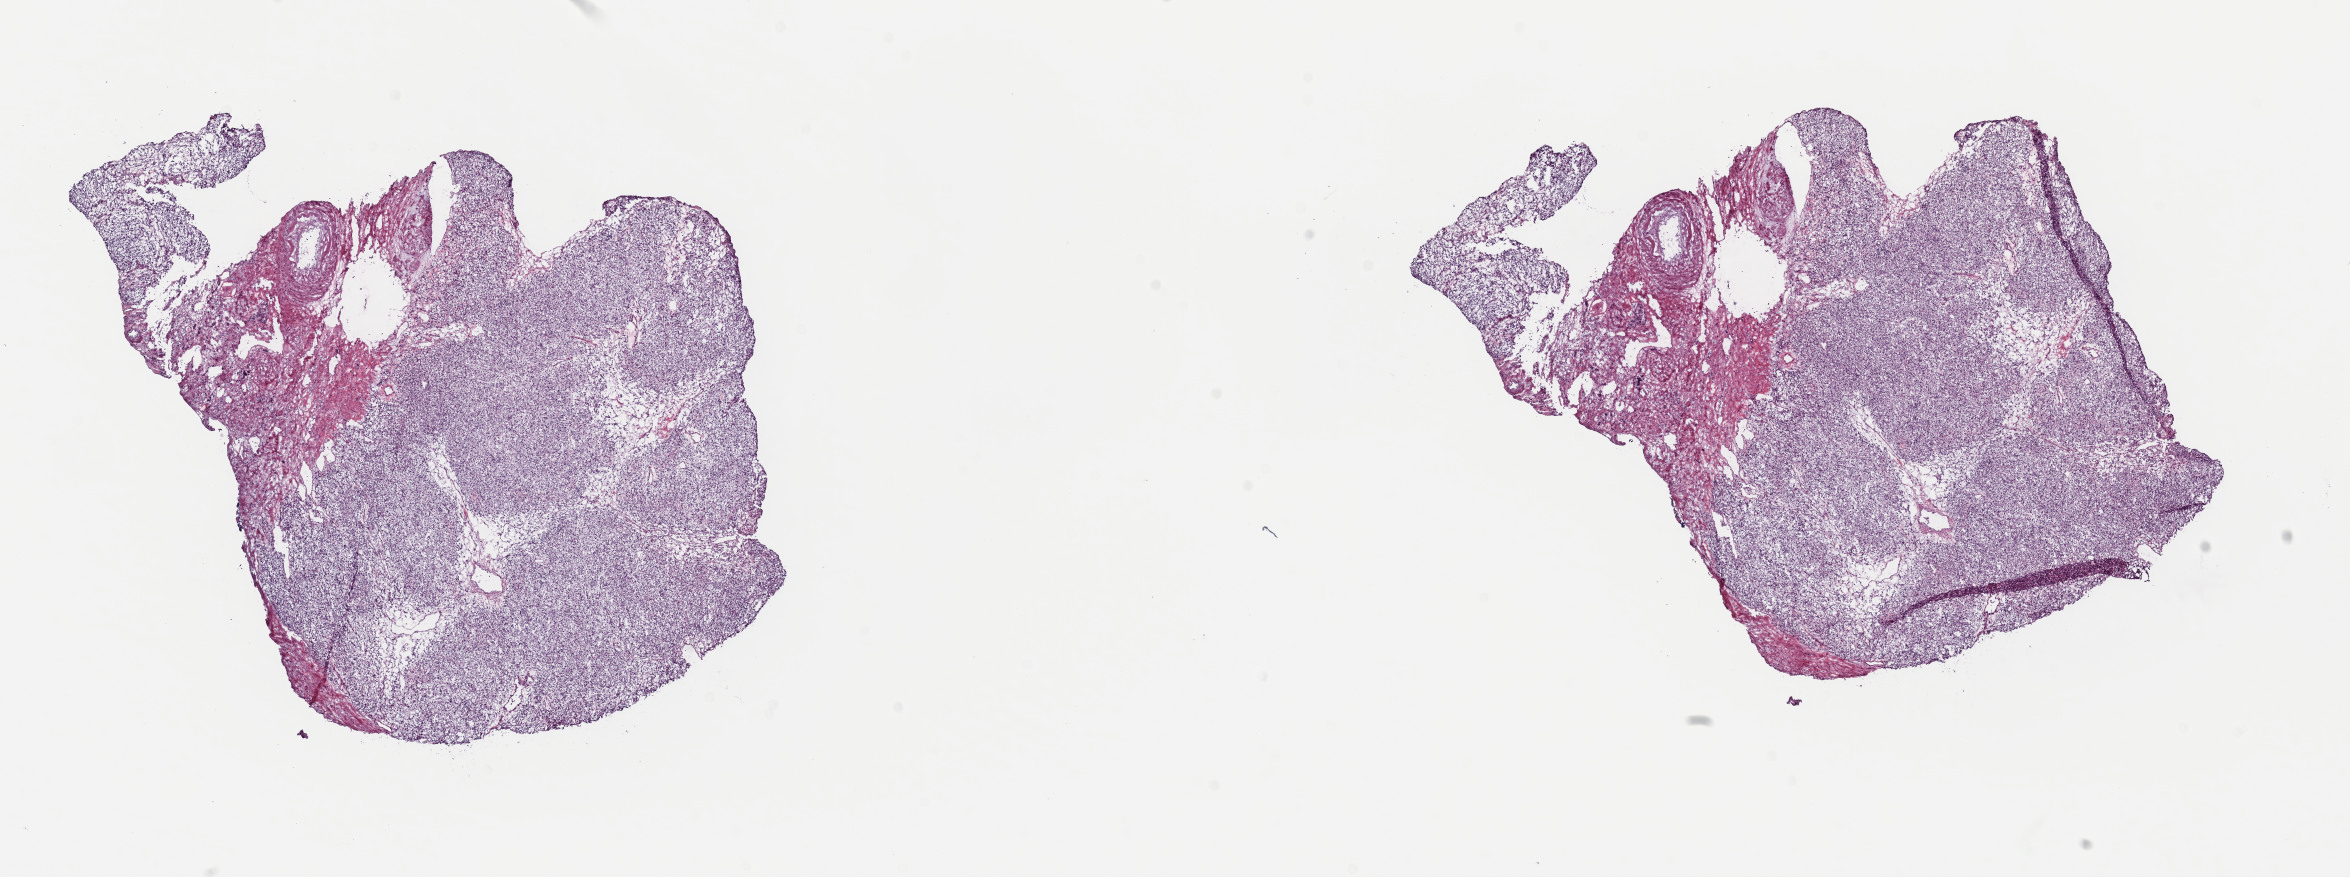
Digitized Hematoxylin and eosin (H&E) stained tissue section (whole slide) — whole scanned area (about 18.6 x 6.9 mm, from a 40x scan) shown as a low-resolution overview; frozen section from the top of the tissue portion; sample: primary tumour, kidney. Female, age 69 years at initial diagnosis. Histologic grade: G3 (poorly differentiated). Pathologist review of this section (percent, as recorded): tumour cells 80%, tumour nuclei 95%, normal cells 0%, stromal cells 20%, necrosis 0%. Infiltration values recorded for this section: lymphocyte infiltration 0%, monocyte infiltration 0%, neutrophil infiltration 0%.
• laterality: left
• AJCC pathologic stage: II
• lymph nodes positive (case pathology): 0 of 2 examined
• histologic diagnosis: Renal cell carcinoma, NOS
• TNM: T2a N0 MX